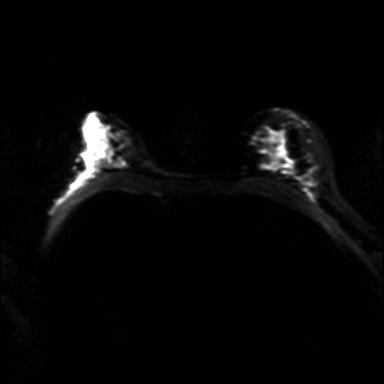
Breast MRI, one axial slice; position 24 of 36 along the scan axis; diffusion-weighted series; image 2 of 4 stored at this slice position (different b-values; order by instance number); 3 T; 4 mm slice thickness; 384 × 384 image matrix. Female patient.
Structures marked on this image (expert manual segmentation):
- tumour on diffusion-weighted imaging: bounding box <110,132,122,142> (left, top, right, bottom; pixels)